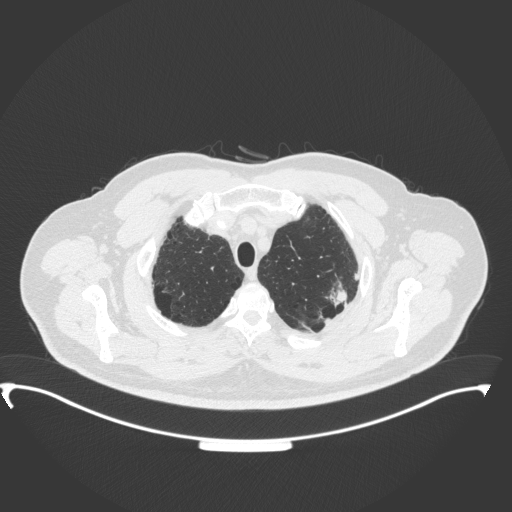
Chest CT, one axial slice. Slice 313 of 350 in the series (ordered by position). Reconstruction kernel B31f. 120 kVp. Lung window (W 1500 / L -600 HU). 1 mm slice thickness. 512 × 512 image matrix. Patient: male, 64 years. Case-level facts recorded for this patient, not image findings: clinical TNM (as recorded): T1c N1 M1.
Annotated regions visible in this slice (rectangle marked by the reading radiologist):
- lung tumour (recorded histology: adenocarcinoma): box from (x=326, y=278) to (x=354, y=314) px